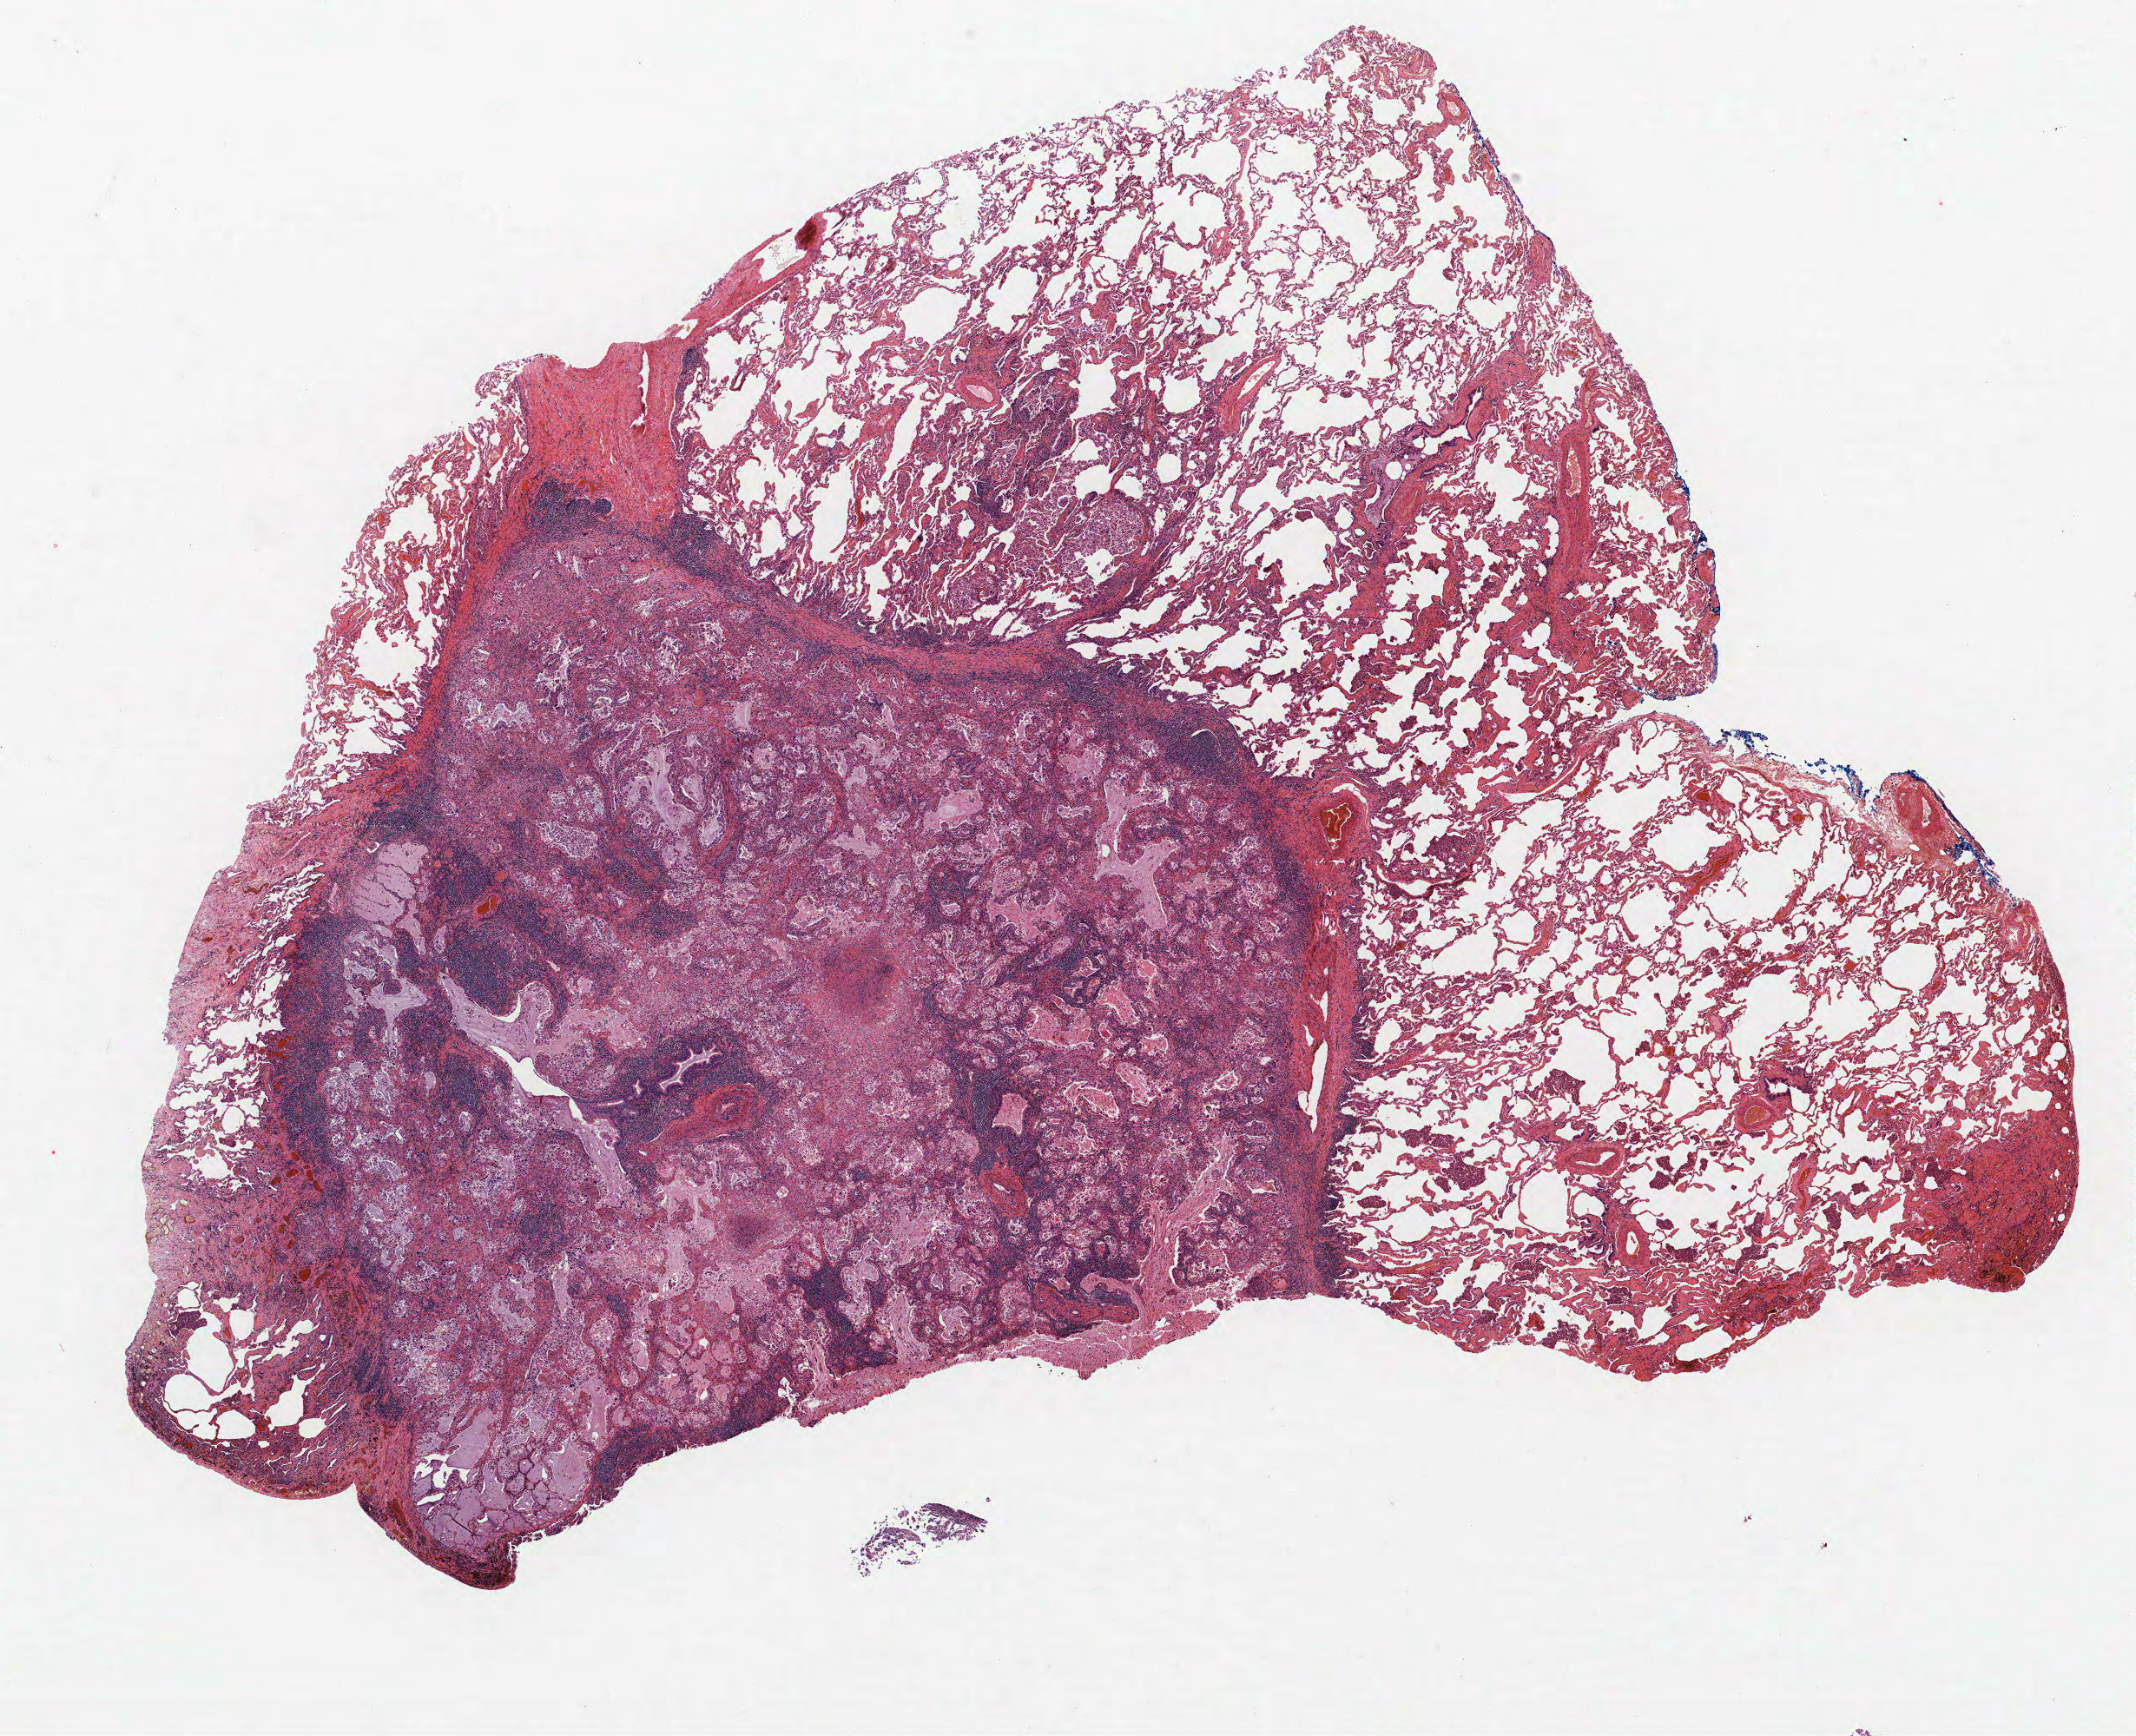
Whole-slide histology image, Hematoxylin and eosin (H&E) stained, low-resolution overview of the scanned area, about 19.7 x 16.0 mm (from a 40x scan); formalin-fixed paraffin-embedded (FFPE) section; lung. Male patient, aged 55 at enrolment. Current smoker at enrolment.
Participant's lung-cancer diagnosis: Mucinous adenocarcinoma.